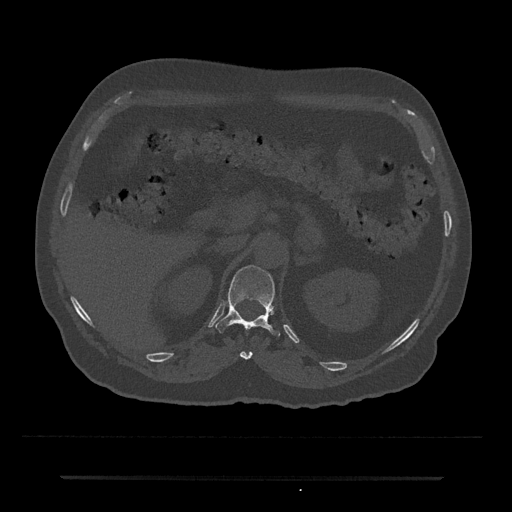
CT including the spine, one axial slice. Slice 132 of 797 in the series (ordered by position). Reconstruction kernel Br40s/3. Bone window (W 1800 / L 400 HU). 512 × 512 image matrix. Patient: male, 69 years. Case-level facts recorded for this patient, not image findings: primary cancer: prostate.
Annotated regions visible in this slice (semi-automatic segmentation, software-assisted and operator-edited):
- T11 vertebra: bounding box [x1, y1, x2, y2] px = [240, 351, 252, 360]
- T12 vertebra: [215, 265, 281, 336]